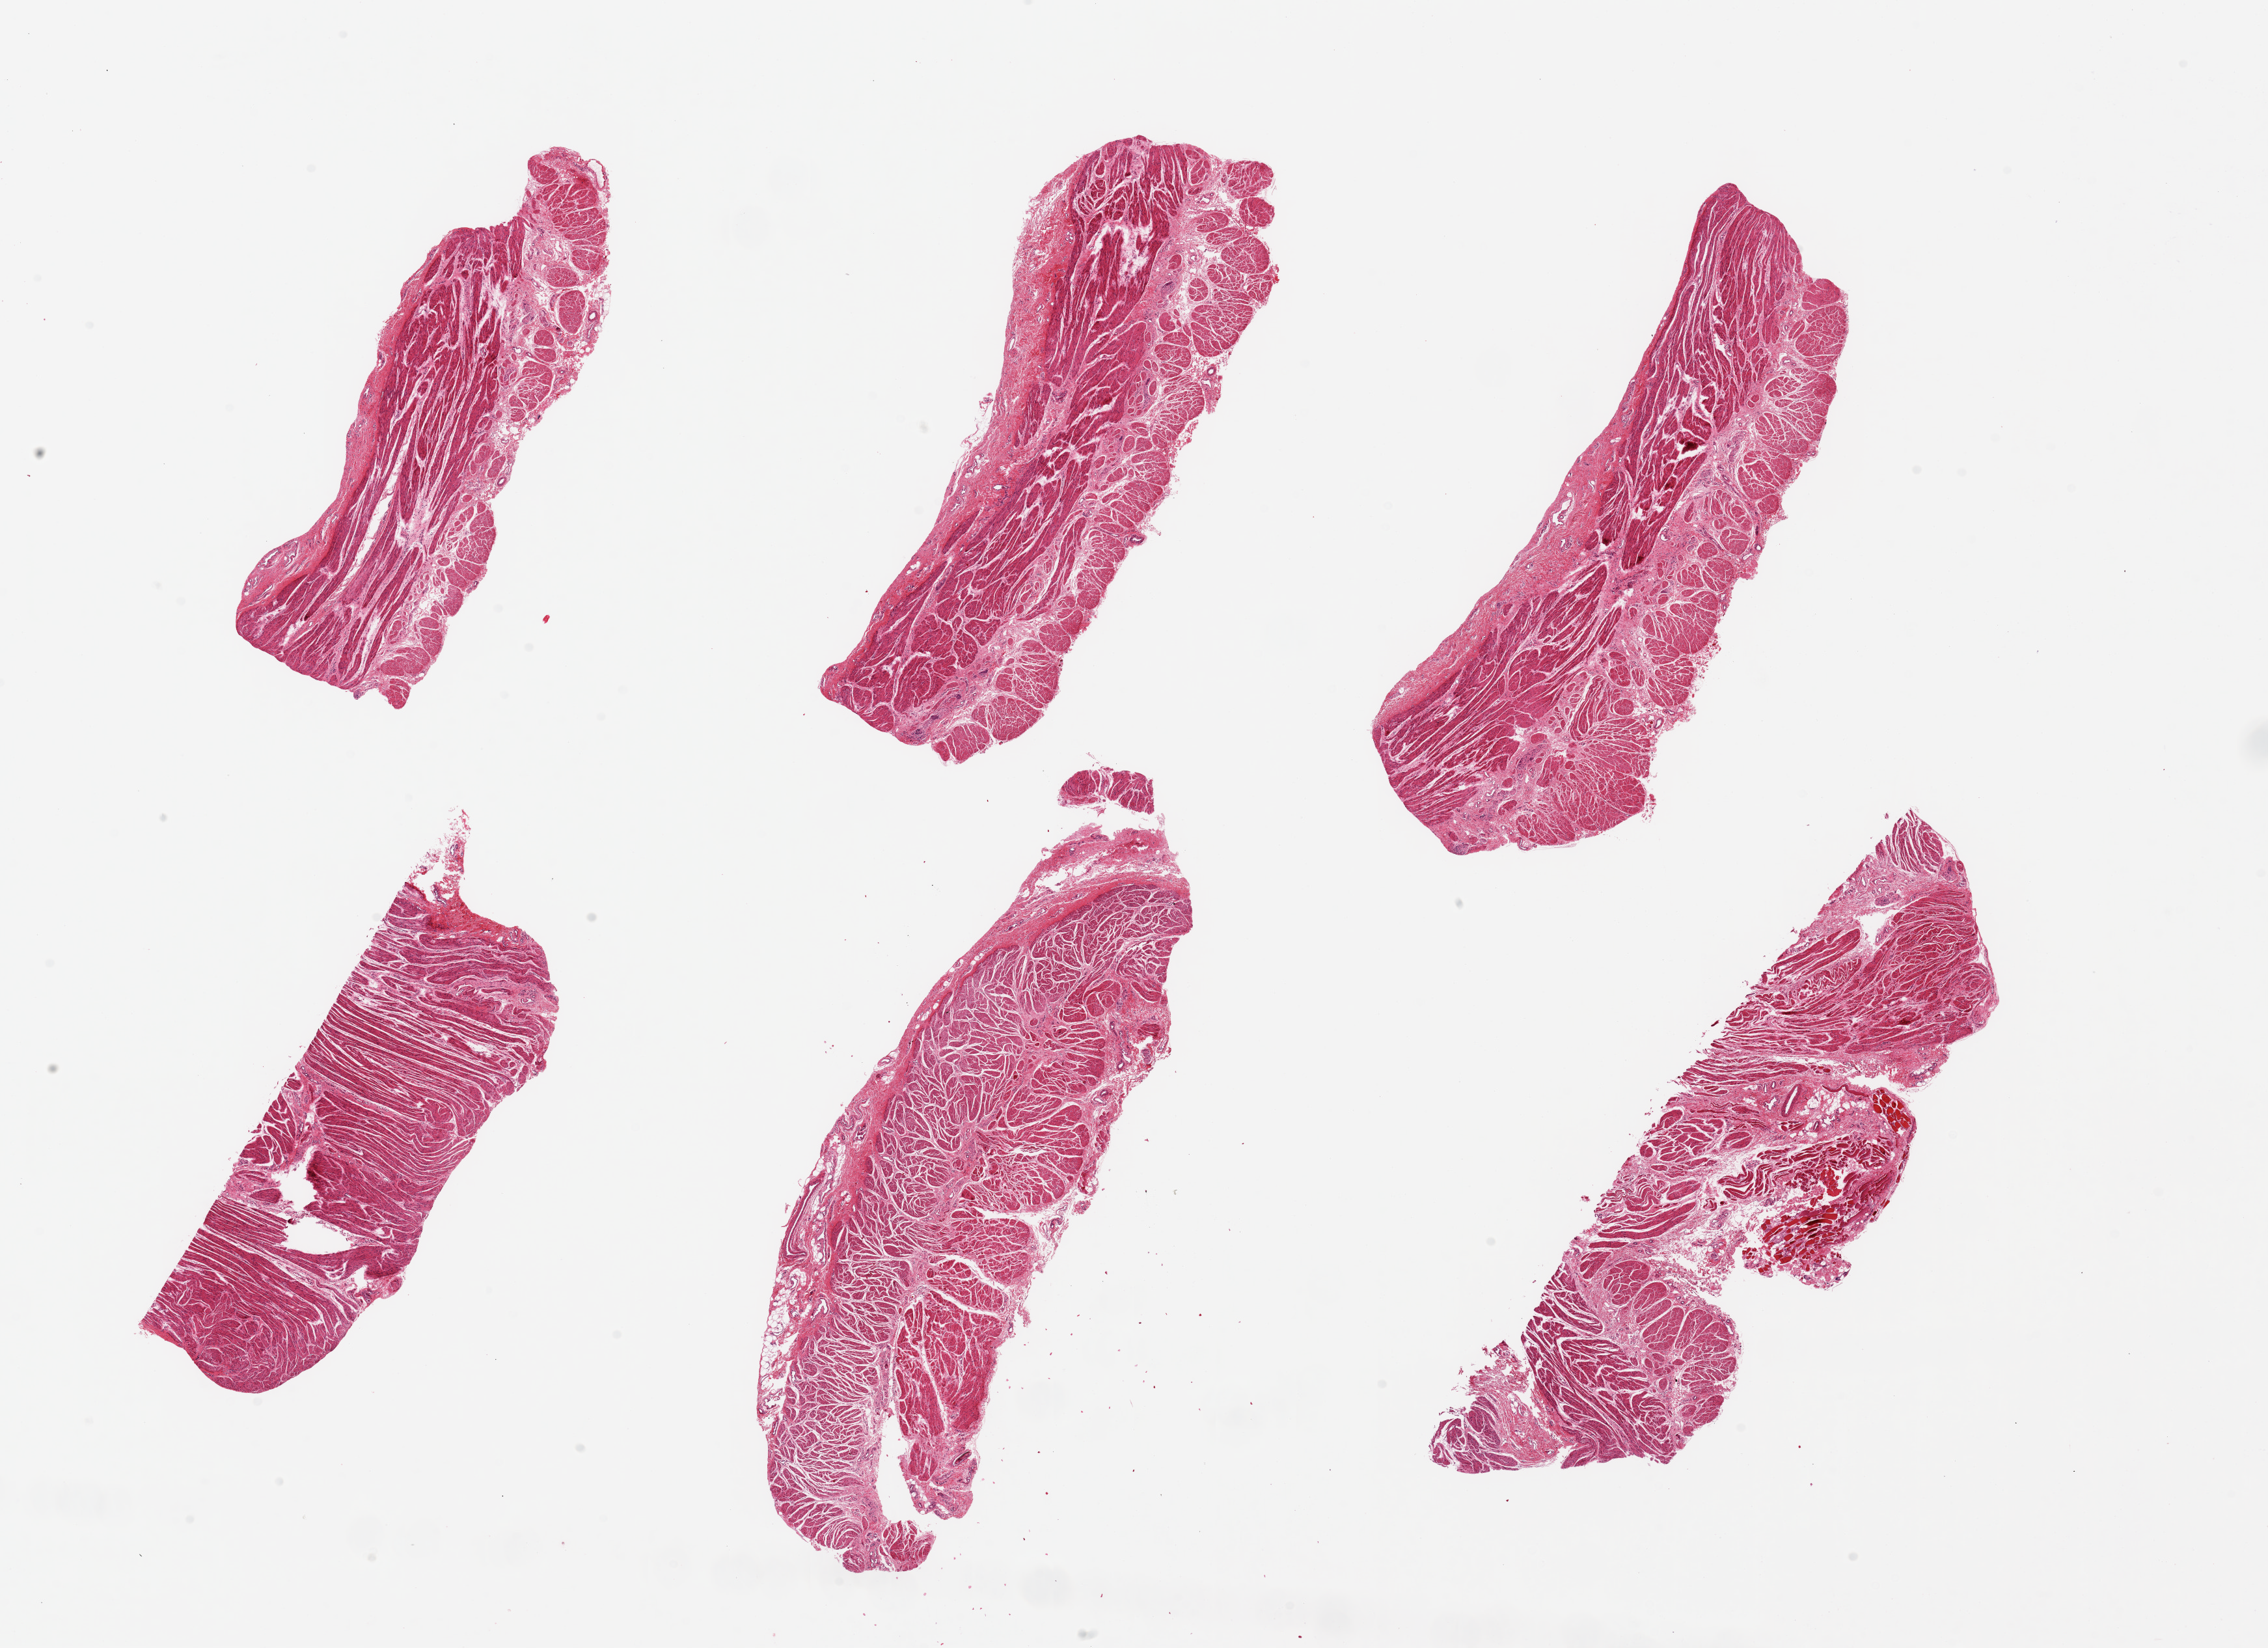
Haematoxylin and eosin whole-slide image — shown as a low-resolution overview of the whole scanned area (about 27.6 x 20.0 mm). PAXgene-fixed, paraffin-embedded tissue. Target tissue: gastroesophageal junction. Donor tissue sample. Donor: male.
Reviewer comment on this tissue sample: 6 pieces ~7x3mm, good specimens, all muscle.